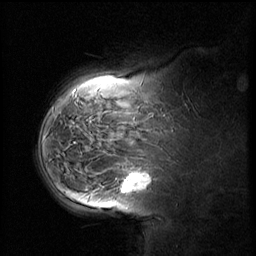
Breast MRI (dynamic contrast-enhanced), one sagittal slice. Position 43 of 58 along the scan axis. Dynamic contrast-enhanced series, image 2 of 2 at this slice position (ordered by acquisition). 1.5 T. TE 4.2 ms, TR 8.9 ms. 3 mm slice thickness. 256 × 256 image matrix, field of view 220 × 220 mm. Patient: female, 37 years. From the clinical record (not read from this slice): setting: breast cancer imaged before/during neoadjuvant chemotherapy; receptor status: triple-negative.
Annotated regions visible in this slice (semi-automatically segmented with operator editing):
- analysis volume of interest (the breast-tissue region the enhancement analysis was run in; not a lesion): bounding box <114,160,164,207> (left, top, right, bottom; pixels)
- tumour enhancement mask (voxels above the 140 % enhancement threshold inside the analysis volume of interest): <124,174,149,191>